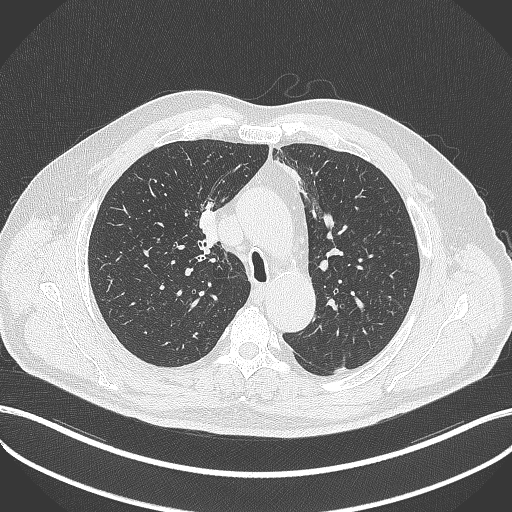
Chest CT, one axial slice; slice 270 of 411 in the series (ordered by position); reconstruction kernel B70f; 120 kVp; lung window (W 1500 / L -600 HU); 1 mm slice thickness; 512 × 512 image matrix. Patient: male, 60 years. From the clinical record (not read from this slice): clinical TNM (as recorded): T1b N1 M0.
Structures marked on this image (rectangle marked by the reading radiologist):
- lung tumour (recorded histology: squamous cell carcinoma): box from (x=193, y=203) to (x=219, y=256) px